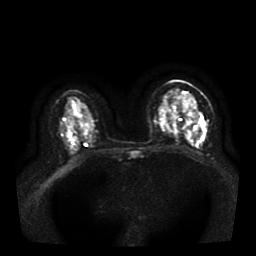
Breast MRI, one axial slice. Slice 21 of 41 in the series (ordered by position). Diffusion-weighted series; image 2 of 4 stored at this slice position (different b-values; order by instance number). 1.5 T. 5 mm slice thickness. 256 × 256 image matrix, field of view 330 × 330 mm. Female patient.
Outlined on this slice (expert manual segmentation):
- tumour on diffusion-weighted imaging: bounding box (x1, y1, x2, y2) in pixels: (186, 112, 203, 138)